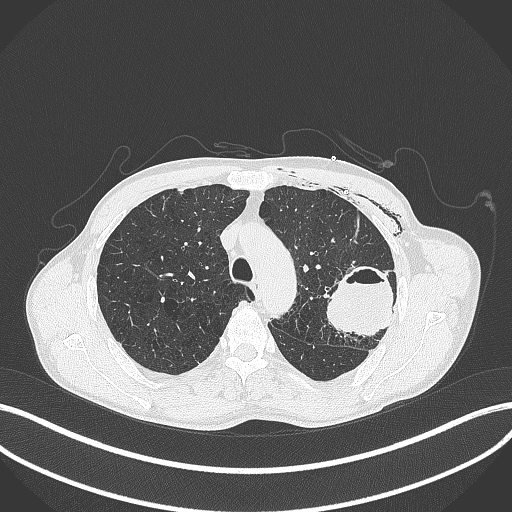
Chest CT, one axial slice. Slice 299 of 457 in the series (ordered by position). Reconstruction kernel B70f. 120 kVp. Lung window (W 1500 / L -600 HU). 1 mm slice thickness. 512 × 512 image matrix, field of view 400 × 400 mm. Male patient, age 58 years. From the clinical record (not read from this slice): clinical TNM (as recorded): T3 N0 M0.
Annotated regions visible in this slice (bounding box drawn by a radiologist):
- lung tumour (recorded histology: adenocarcinoma): bounding box [x1, y1, x2, y2] px = [323, 263, 400, 337]